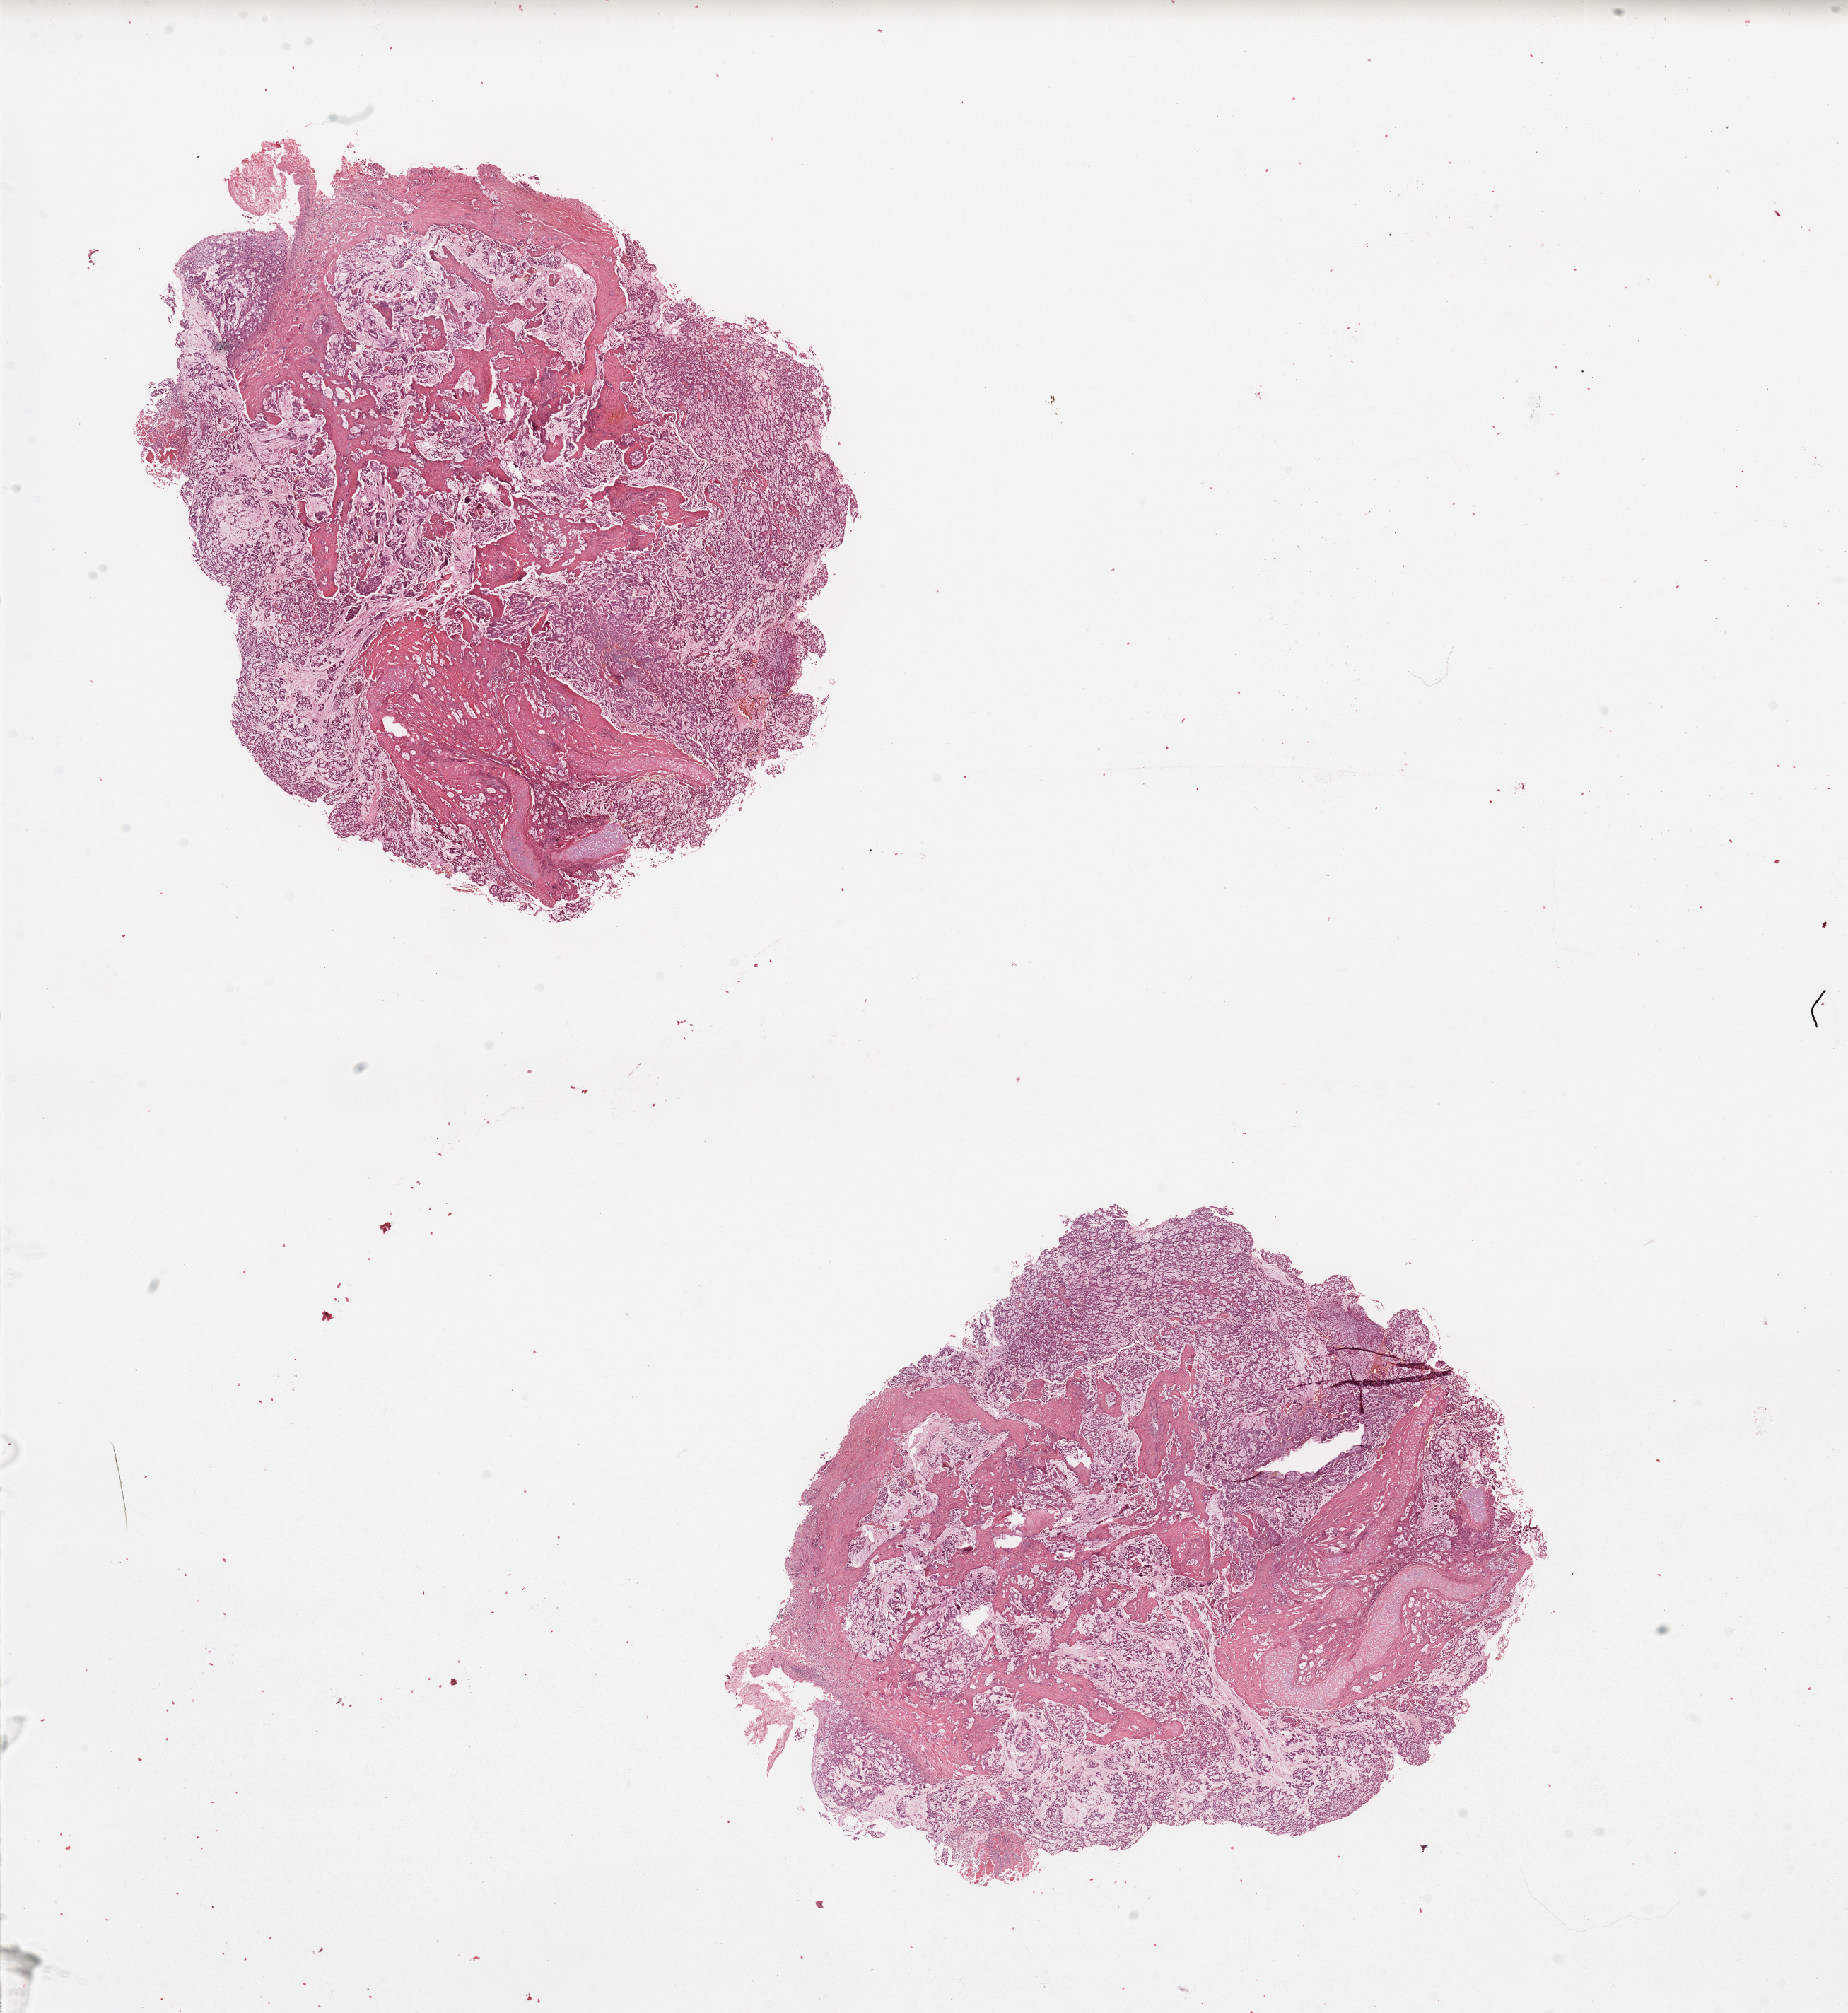
Hematoxylin and eosin (H&E) stained whole-slide image, a low-resolution overview of the entire scanned area, about 20.7 x 22.5 mm, tumour tissue sample, sampled site: lung. Female, 36 y/o. Histologic grade: G2 (moderately differentiated). Slide review estimates, as recorded: tumour nuclei 70%, necrosis 3%.
* AJCC pathologic stage: IIIA
* primary tumour site (as recorded): left upper lobe
* diagnosis: Adenocarcinoma, NOS